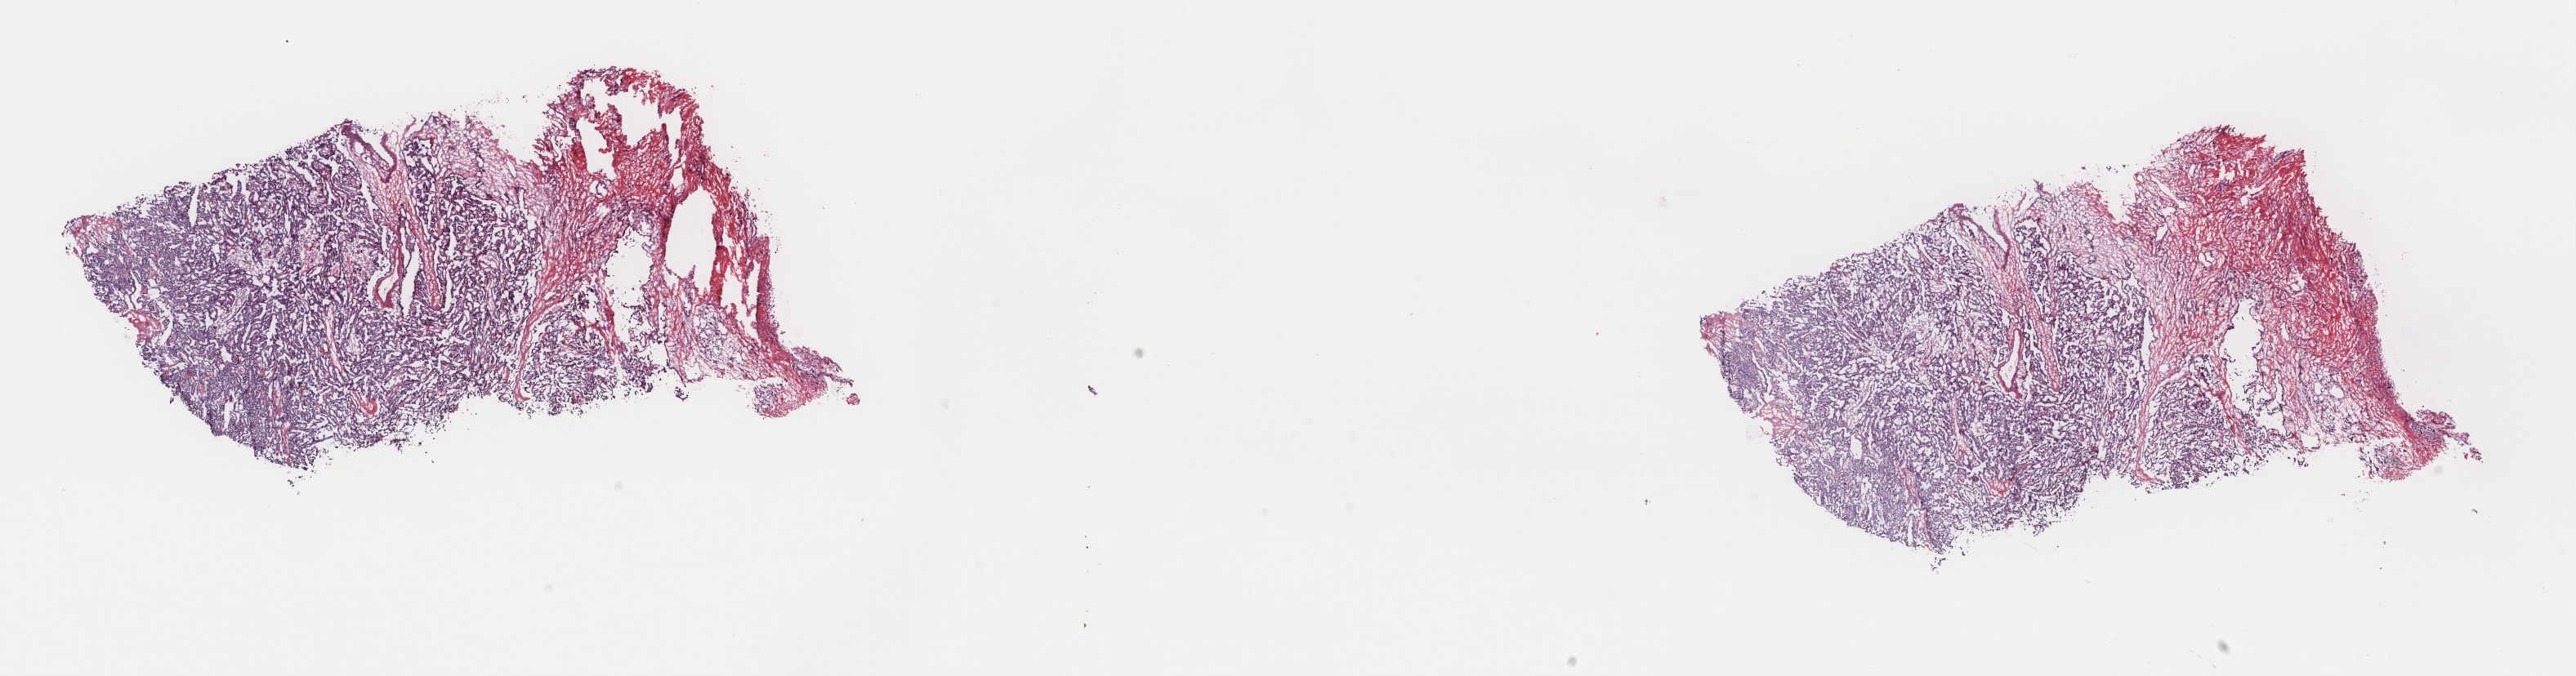
Digitized Hematoxylin and eosin (H&E) stained tissue section (whole slide), whole scanned area (about 25.0 x 6.6 mm, from a 40x scan) shown as a low-resolution overview, frozen section from the top of the tissue portion, sample: primary tumour, thyroid. Female, age 50 years at initial diagnosis. Pathologist review of this section (percent, as recorded): tumour cells 85%, tumour nuclei 85%, normal cells 0%, stromal cells 15%, necrosis 0%. Infiltration values recorded for this section: lymphocyte infiltration 0%, monocyte infiltration 0%, neutrophil infiltration 0%.
Lymph nodes positive (case pathology): 0 of 3 examined. AJCC pathologic stage: I. TNM: T1b N0 M0. Pathologic diagnosis: Papillary adenocarcinoma, NOS (thyroid gland).